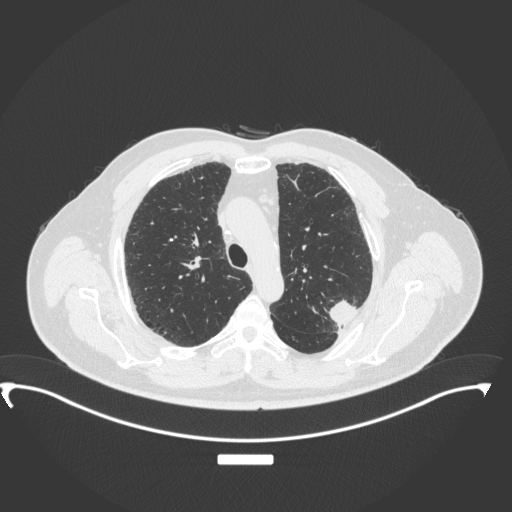
Chest CT, one axial slice; slice 264 of 350 in the series (ordered by position); reconstruction kernel B31f; 120 kVp; lung window (W 1500 / L -600 HU); 1 mm slice thickness; 512 × 512 image matrix. Patient: male, 64 years. Case-level facts recorded for this patient, not image findings: clinical TNM (as recorded): T1c N1 M1.
Outlined on this slice (bounding box drawn by a radiologist):
- lung tumour (recorded histology: adenocarcinoma): bounding box (x1, y1, x2, y2) in pixels: (323, 293, 360, 330)